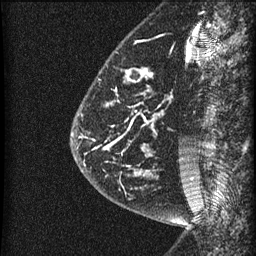
Breast MRI (dynamic contrast-enhanced), one sagittal slice; position 15 of 60 along the scan axis; dynamic contrast-enhanced series, image 2 of 3 at this slice position (ordered by acquisition); 1.5 T; TE 4.2 ms, TR 22.7 ms; 1.5 mm slice thickness; 256 × 256 image matrix. Female patient, age 48 years. Case-level facts recorded for this patient, not image findings: setting: breast cancer imaged before/during neoadjuvant chemotherapy; receptor status: triple-negative.
Annotated regions visible in this slice (semi-automatic segmentation, software-assisted and operator-edited):
- analysis volume of interest (the breast-tissue region the enhancement analysis was run in; not a lesion): bounding box (x1, y1, x2, y2) in pixels: (81, 23, 186, 202)
- tumour enhancement mask (voxels above the 90 % enhancement threshold inside the analysis volume of interest): (81, 69, 148, 175)